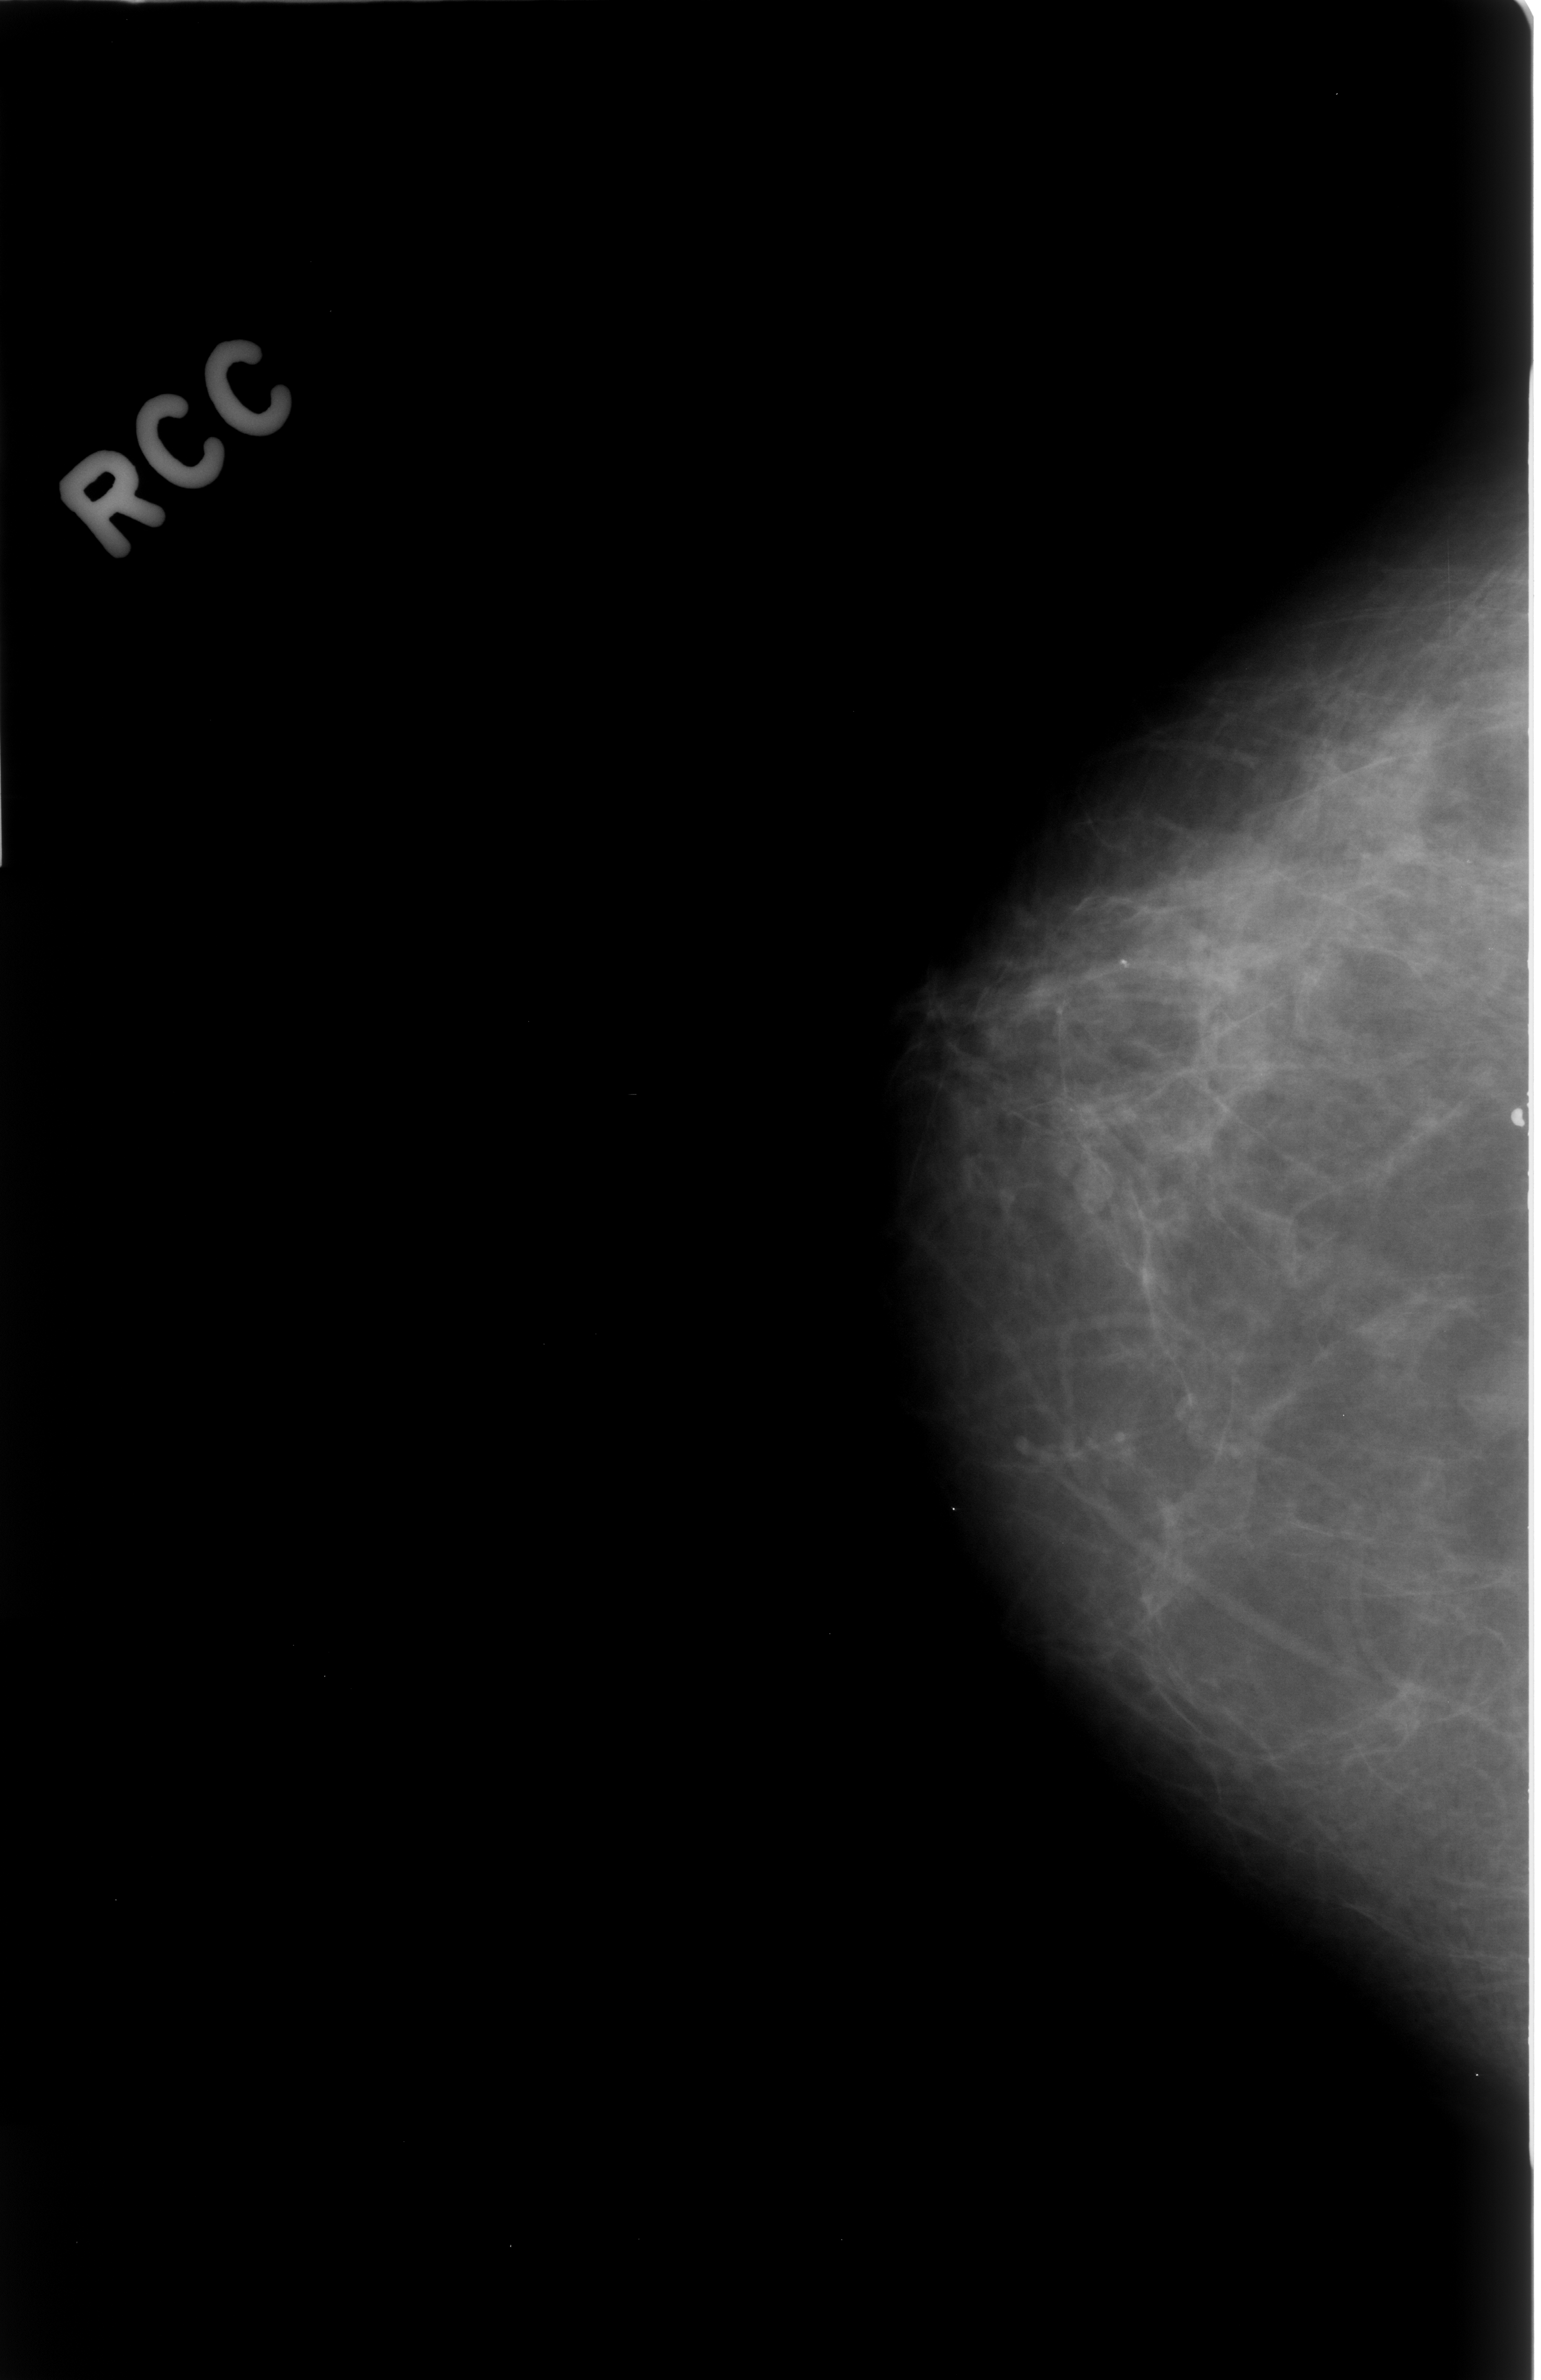
Scanned film-screen mammogram; right breast; craniocaudal (CC) view; breast composition: scattered fibroglandular densities (BI-RADS density category 2 of 4); 1541 × 2380 image matrix.
Expert-marked regions of interest on this film, with their recorded descriptors:
- mass, shape round, margins circumscribed; BI-RADS assessment category 3; outcome (as recorded, no biopsy): benign without callback (not worked up further): bounding box (x1, y1, x2, y2) in pixels: (1464, 1335, 1541, 1469)